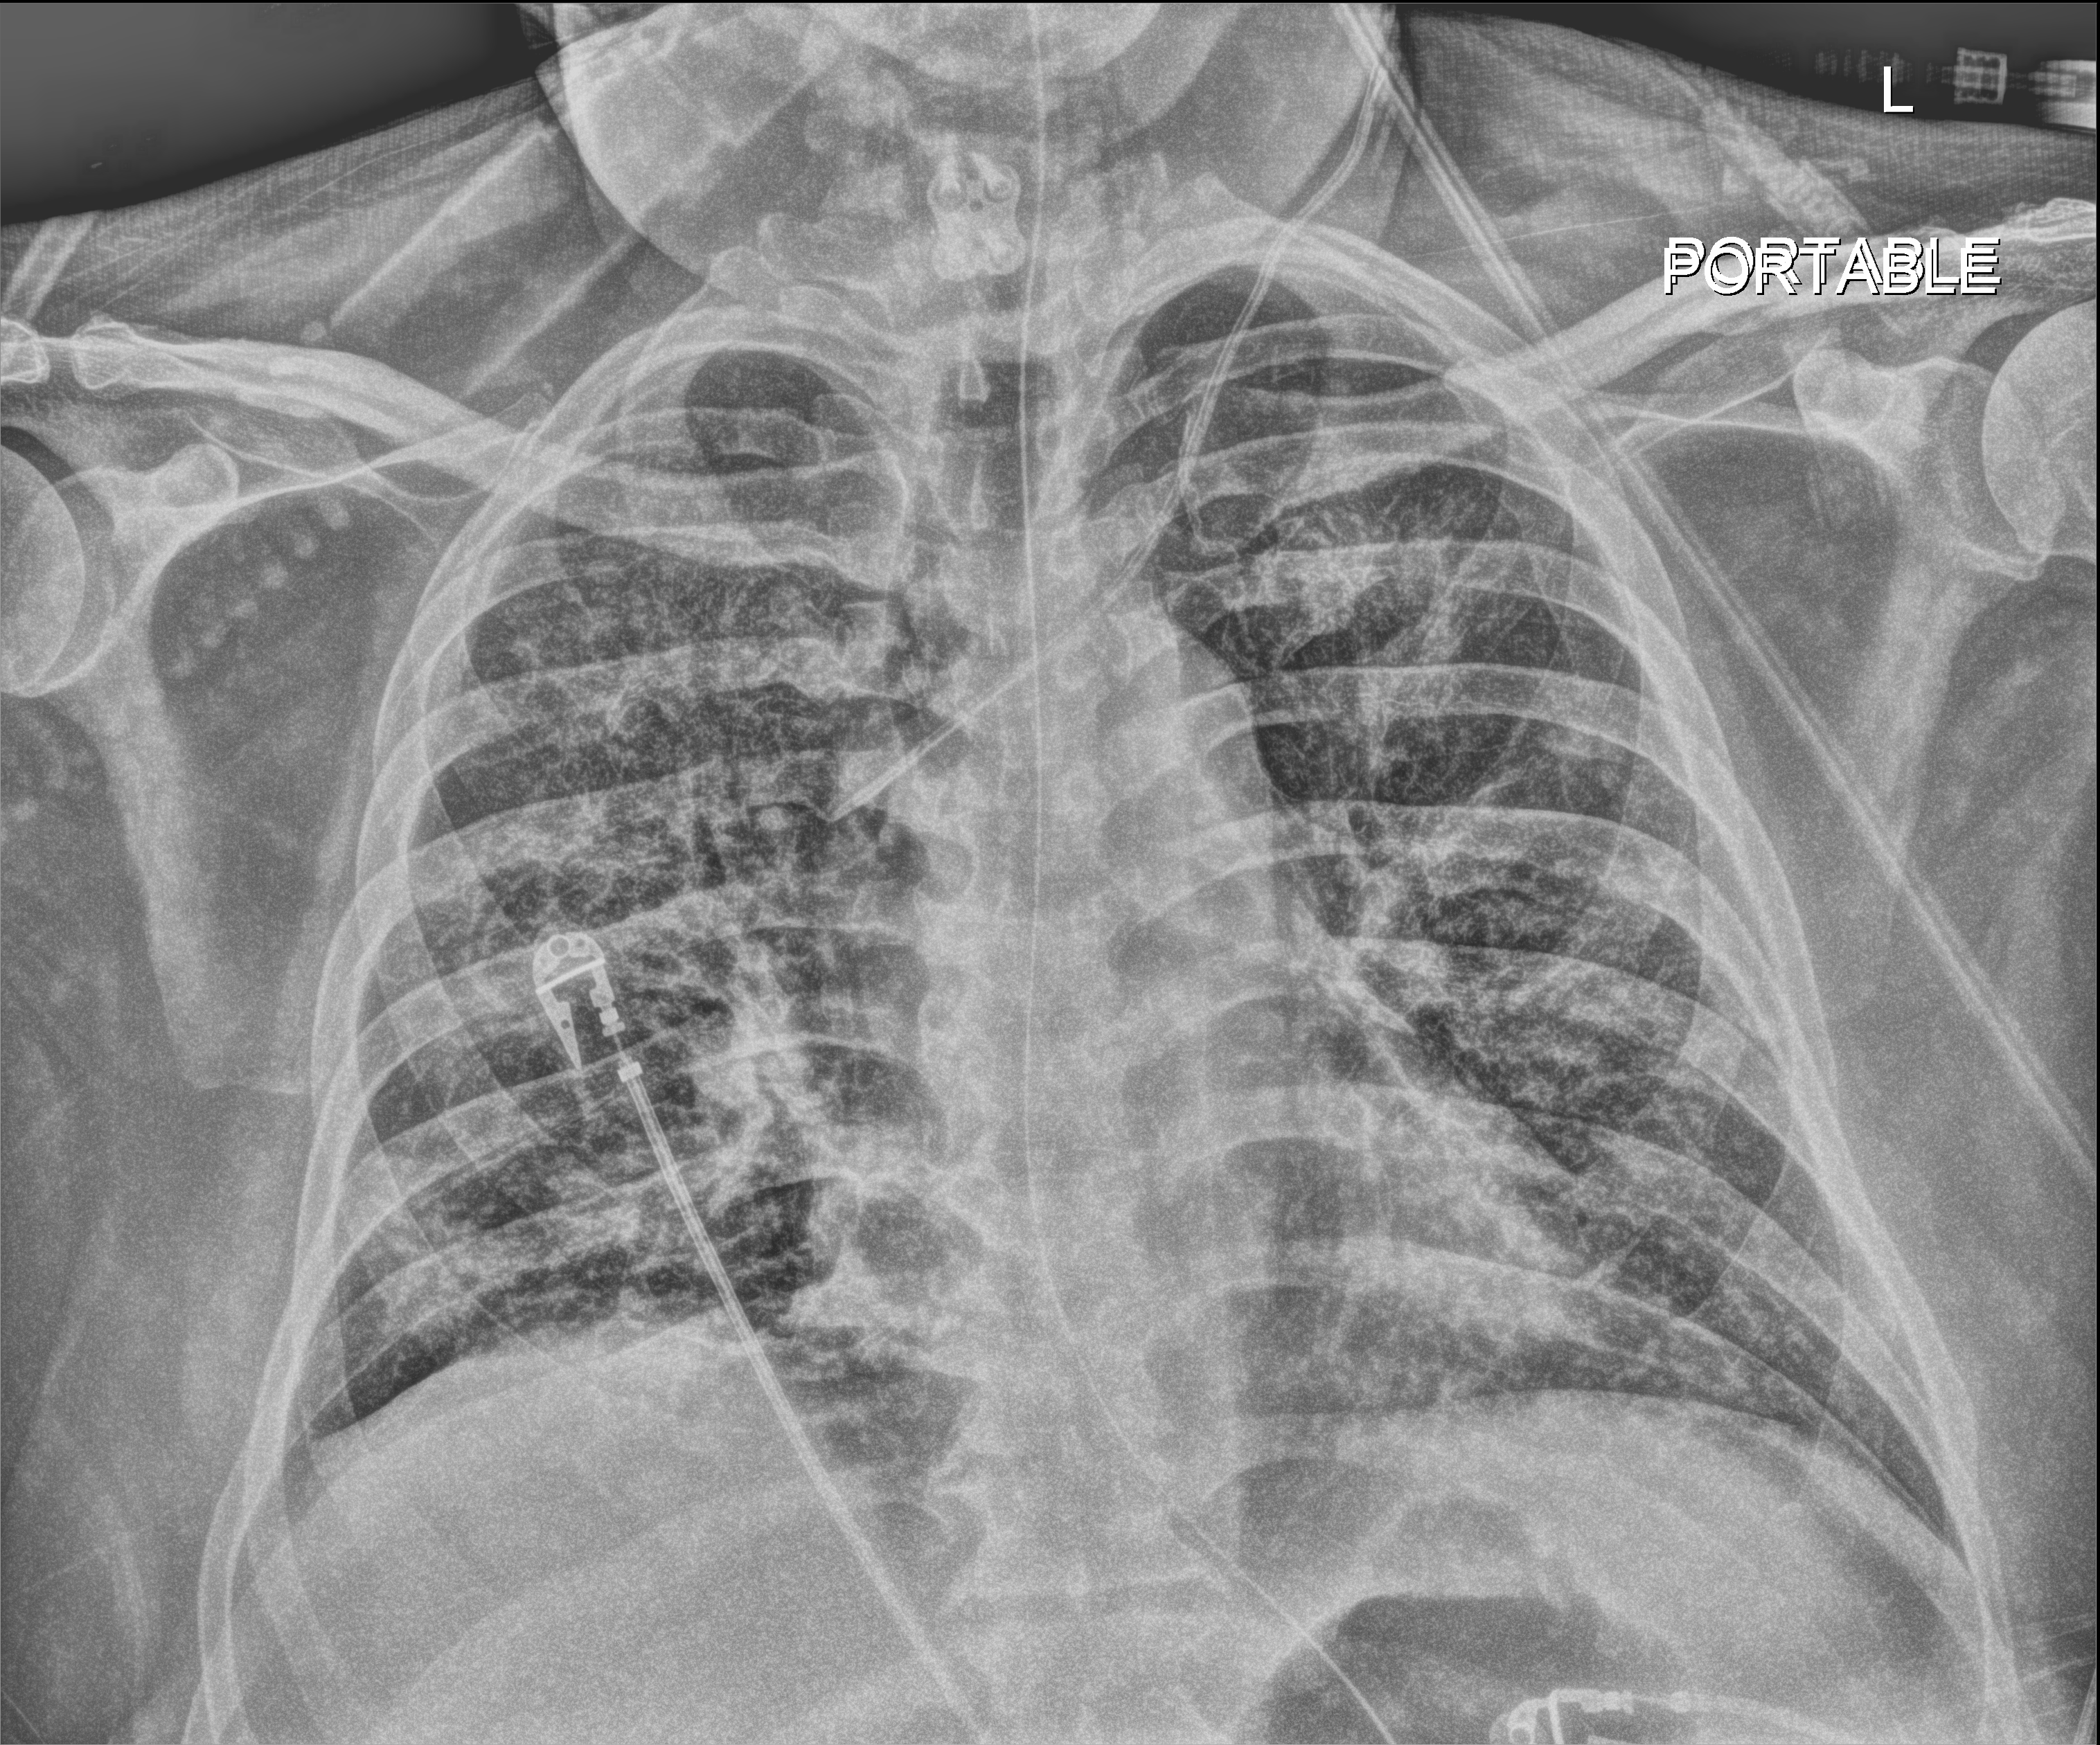
Chest X-ray (portable); anteroposterior (AP) projection. Patient hospitalised with COVID-19; male, aged 18–59 years.
From the hospital-stay record, not from the radiograph (when in the stay this image was taken is not recorded): diabetes (admission record): no.